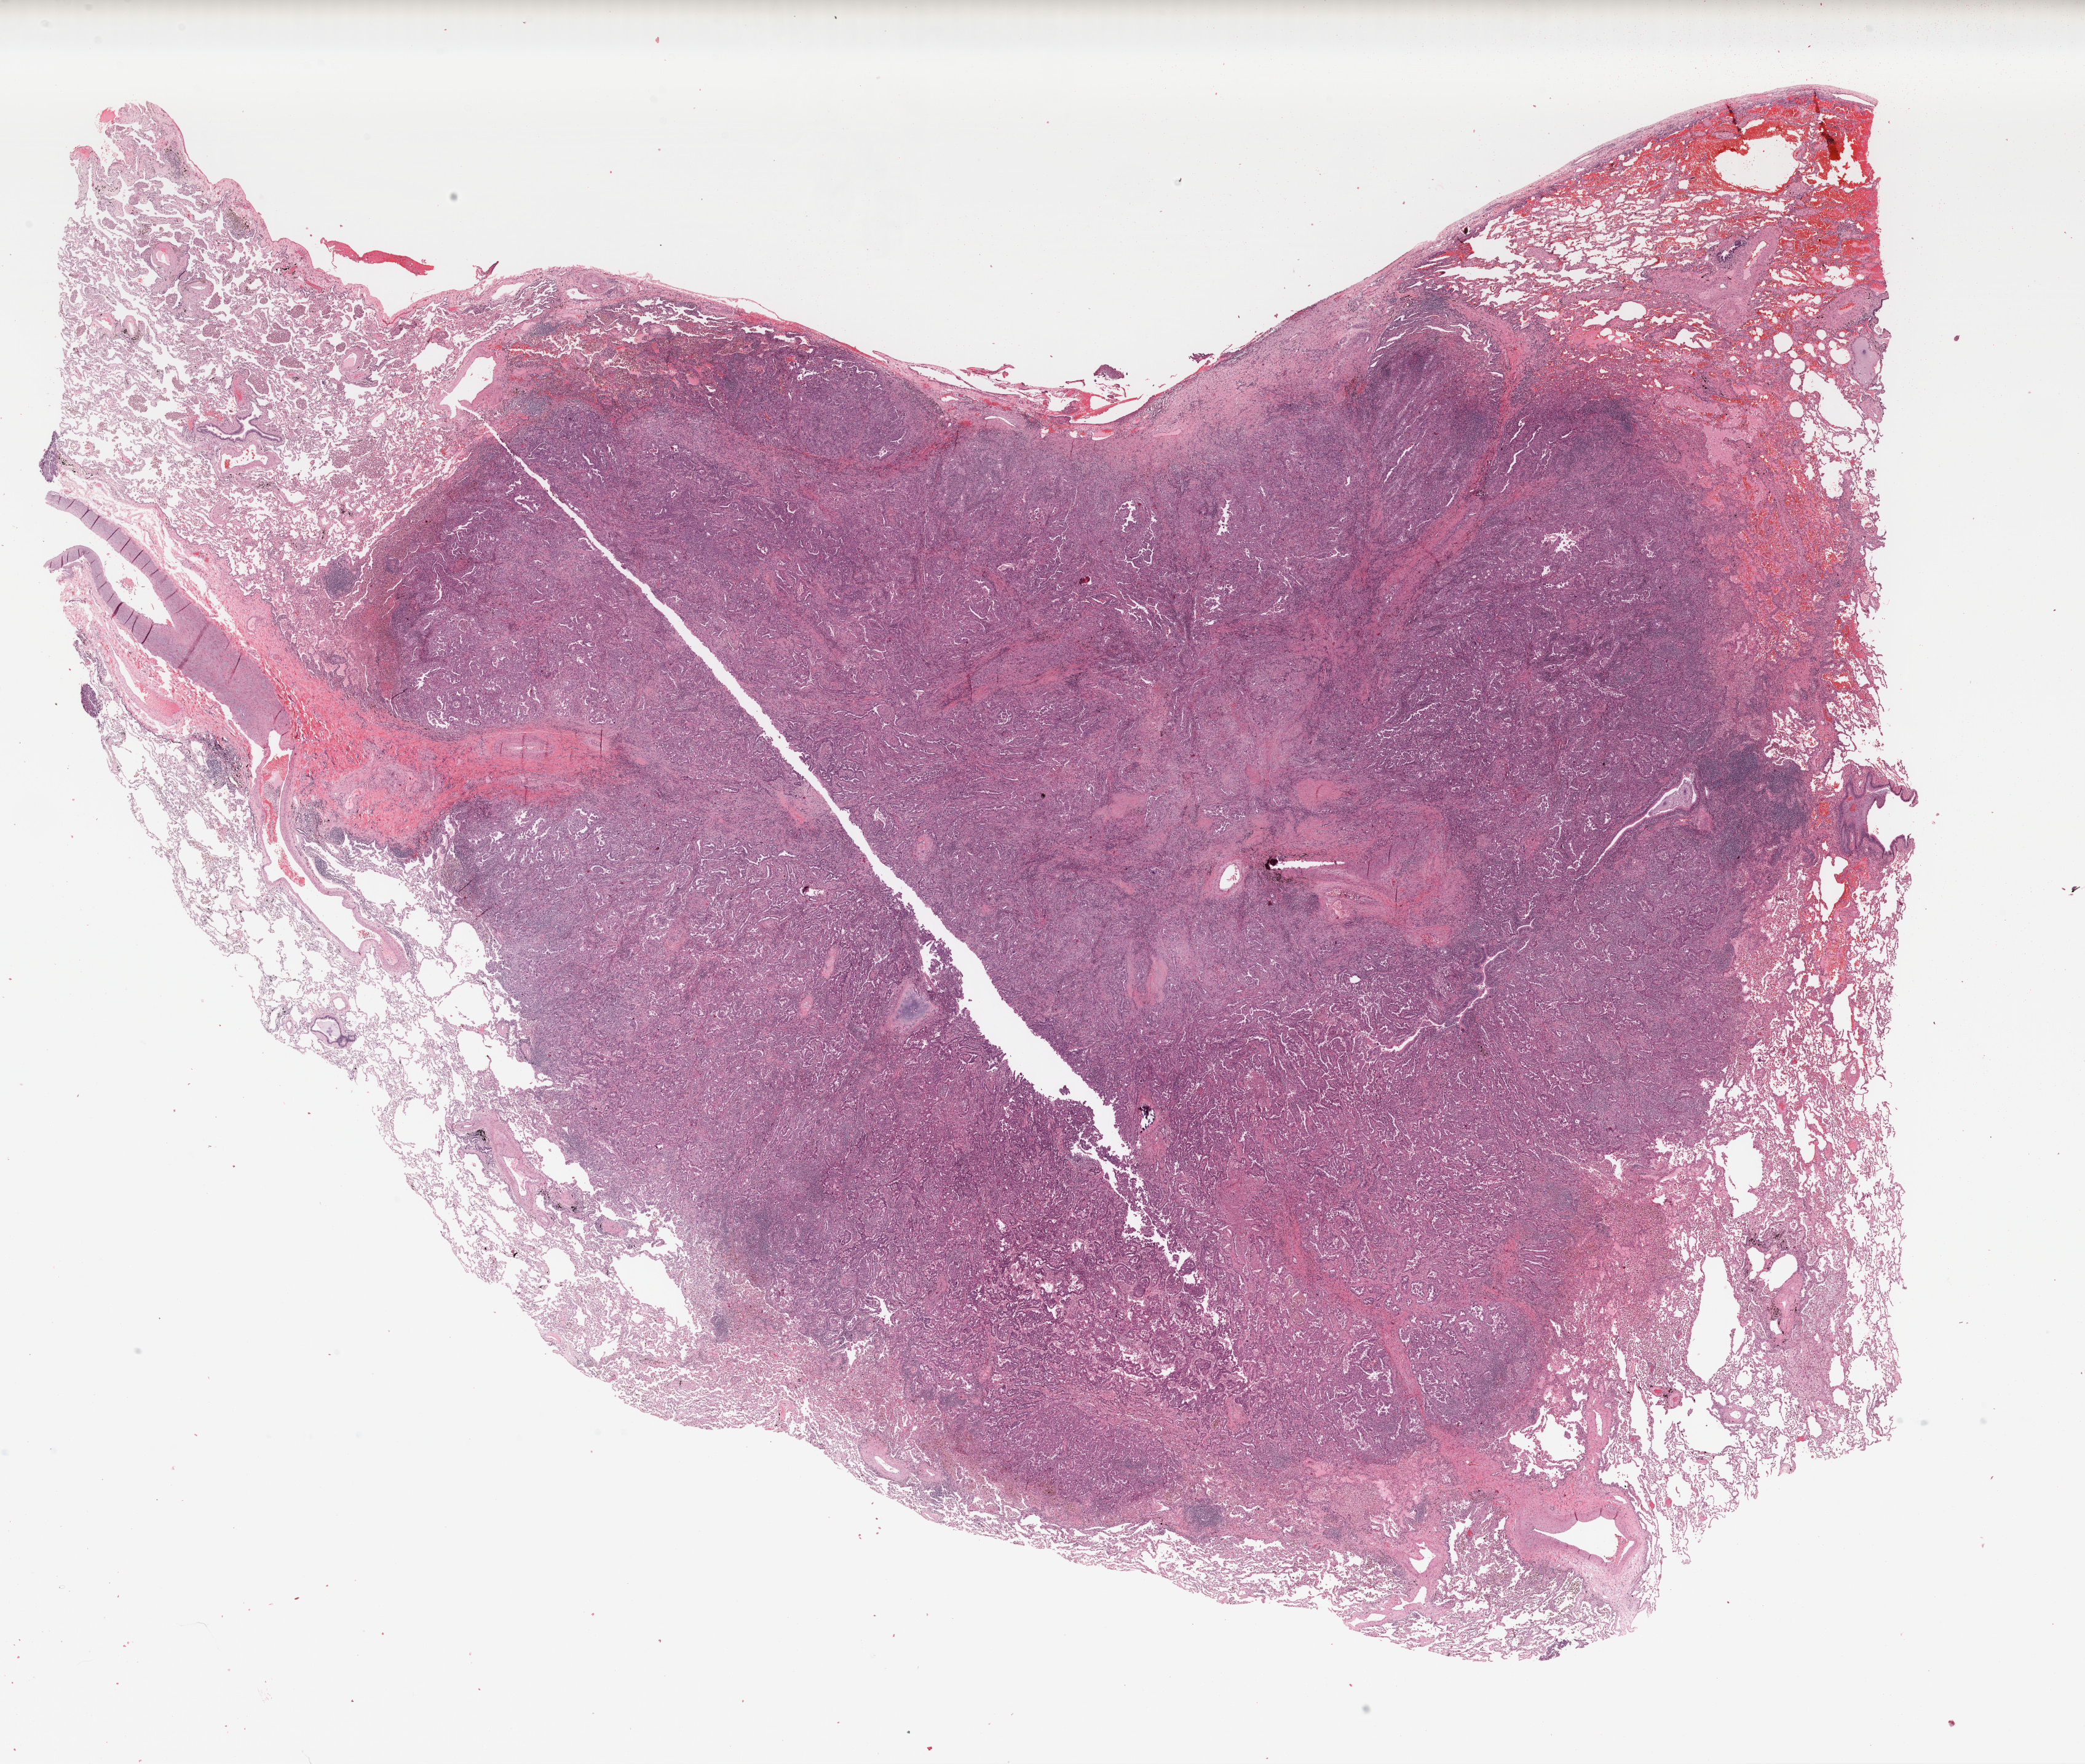
Digitized Hematoxylin and eosin (H&E) stained tissue section (whole slide) — whole scanned area (about 26.7 x 22.6 mm) shown as a low-resolution overview. Formalin-fixed paraffin-embedded (FFPE) diagnostic section. Primary tumour sample from the lung. Female patient; age at initial diagnosis 48 years.
AJCC pathologic stage: I (7th edition). Laterality: left. Pathologic diagnosis: Adenocarcinoma, NOS (upper lobe, lung).